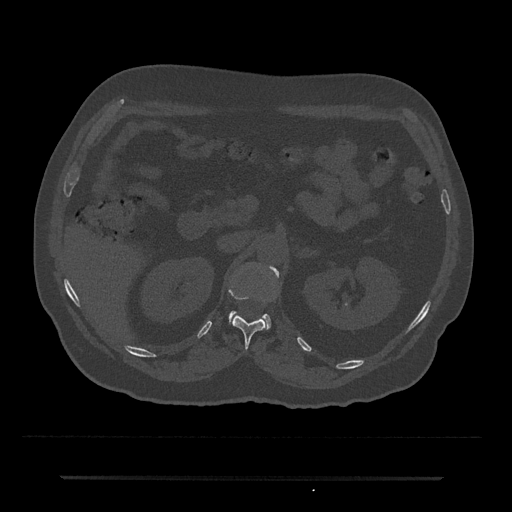
CT including the spine, one axial slice; slice 110 of 797 in the series (ordered by position); 120 kVp; bone window (W 1800 / L 400 HU); 512 × 512 image matrix. Patient: male, 69 years. Case-level facts recorded for this patient, not image findings: primary cancer: prostate.
Structures marked on this image (semi-automatically segmented with operator editing):
- L1 vertebra: box from (x=229, y=266) to (x=279, y=328) px
- T12 vertebra: (x=228, y=286)–(x=267, y=348)